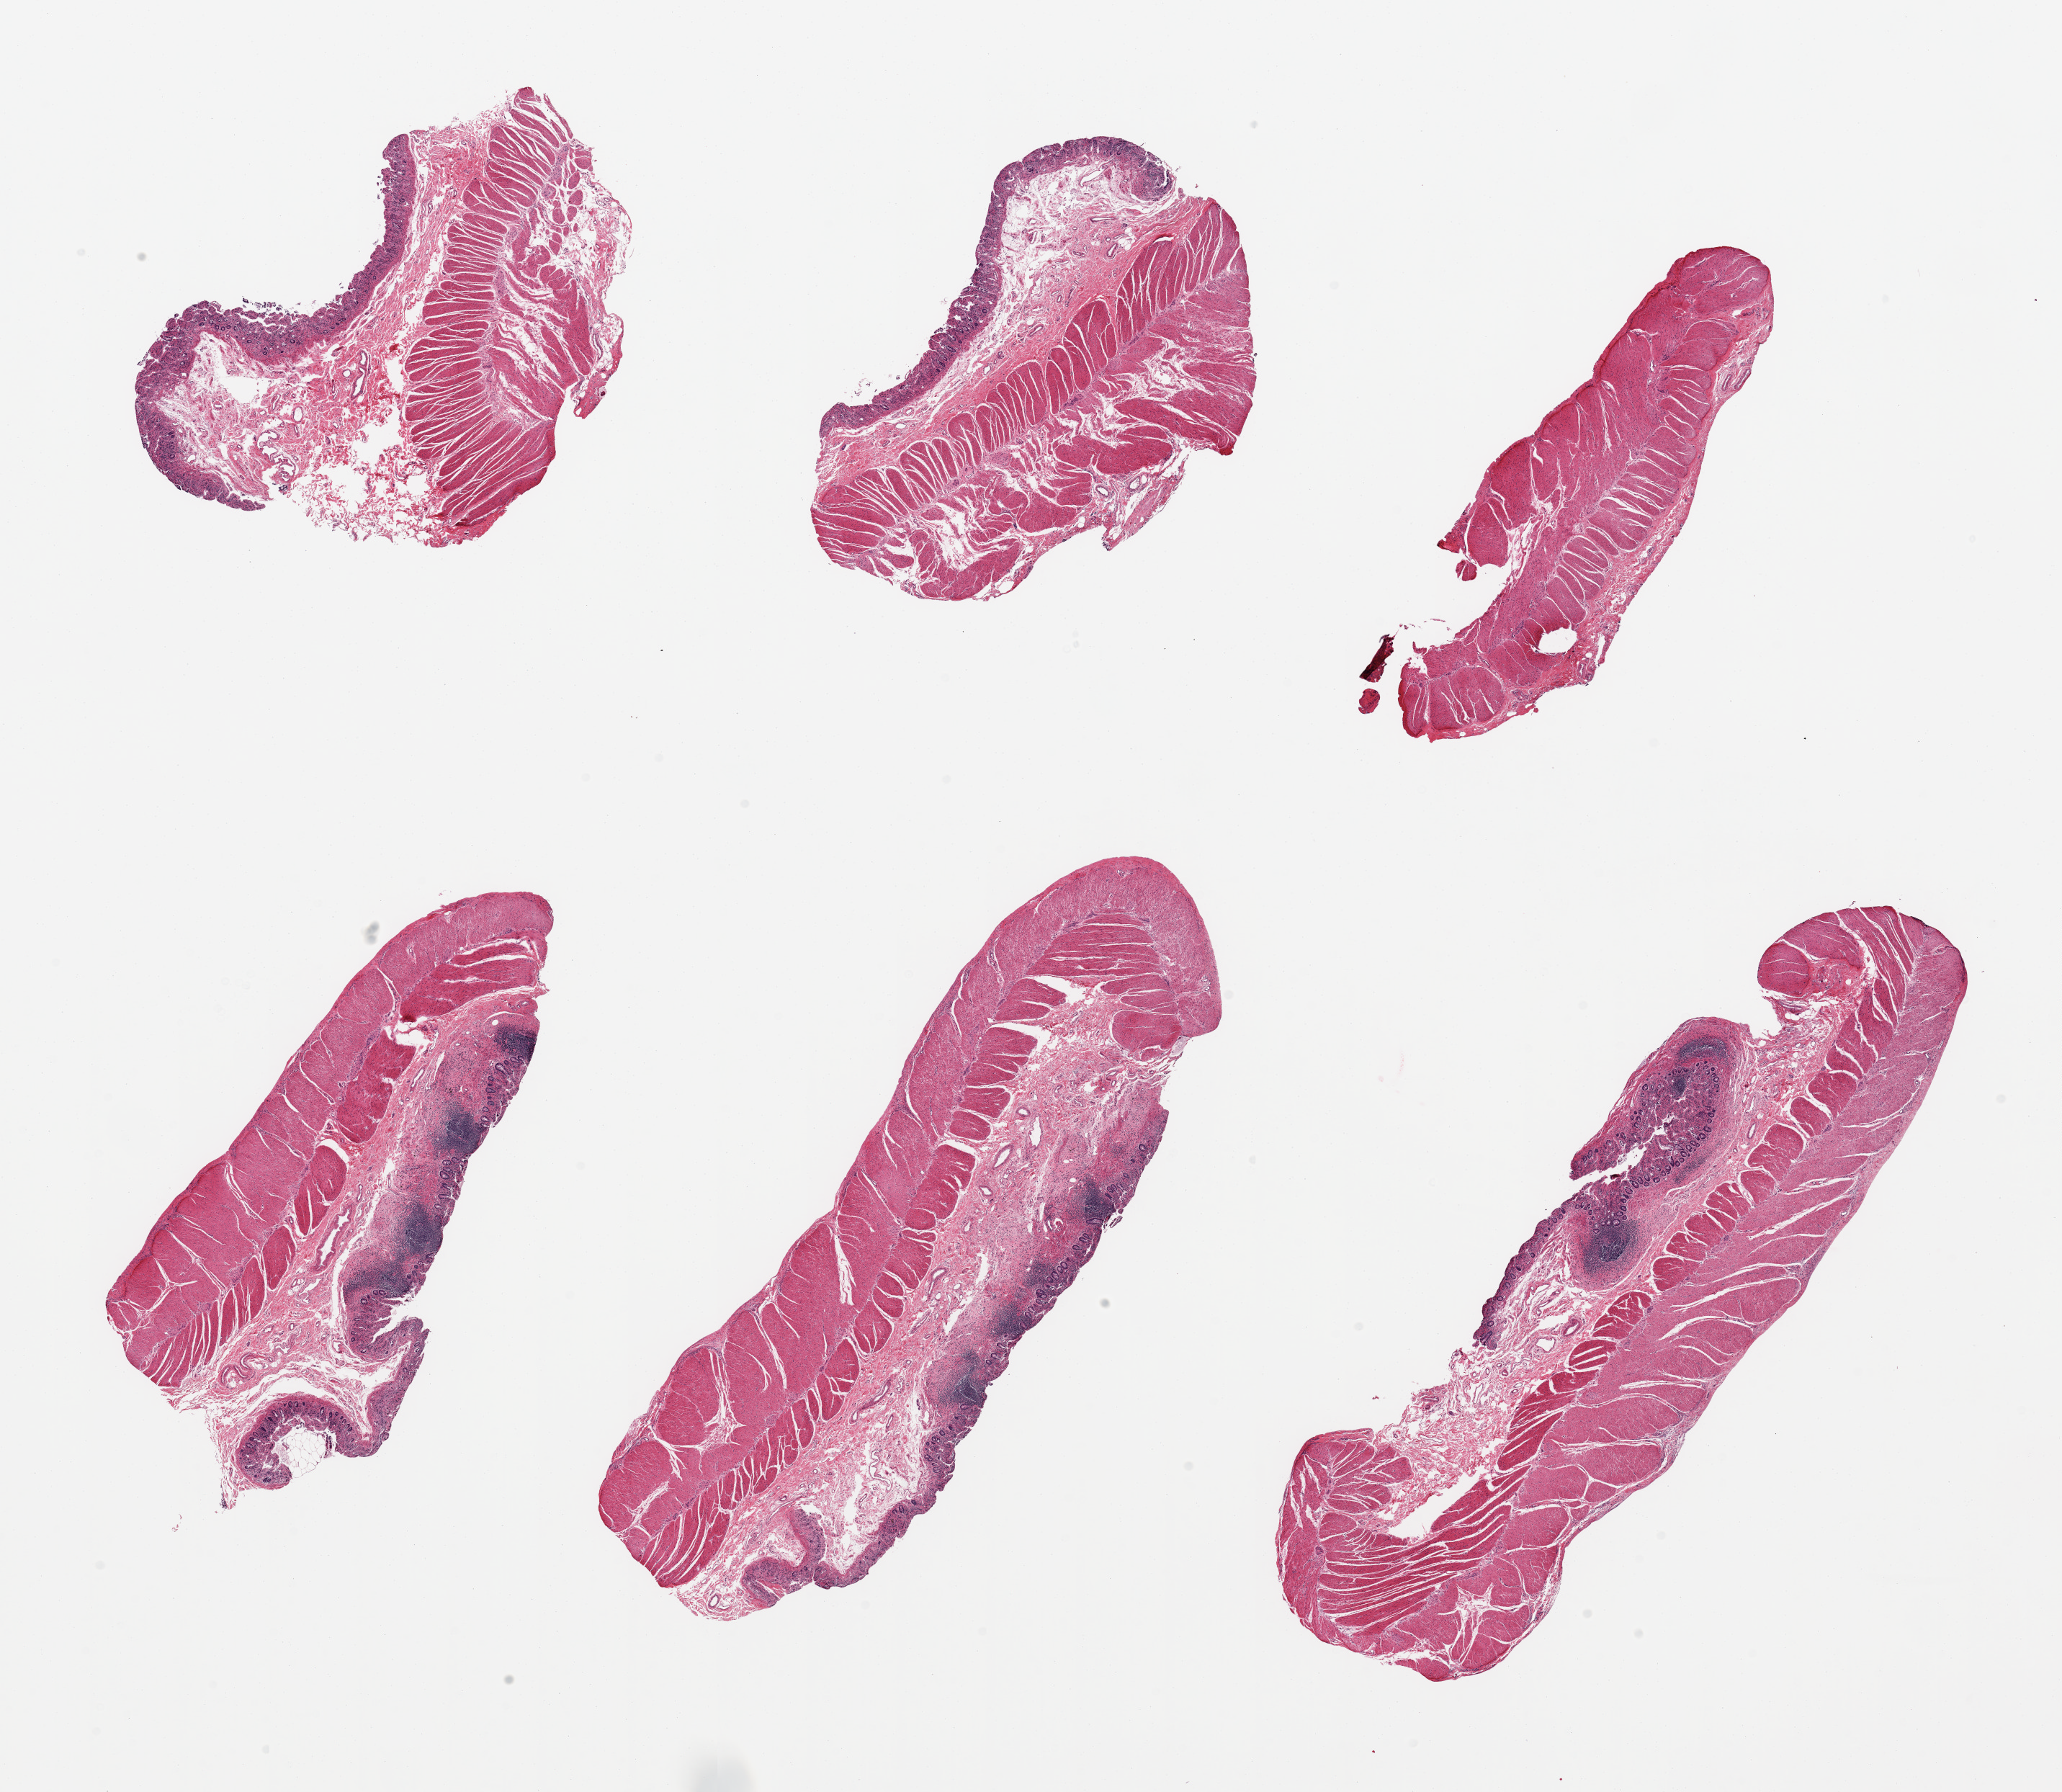
Whole-slide image, H&E stain, shown as a low-resolution overview of the whole scanned area (about 22.6 x 19.7 mm). Donor sex: female.
* specimen: PAXgene-fixed paraffin-embedded (PFPE) section; target tissue: ileum; donor tissue sample